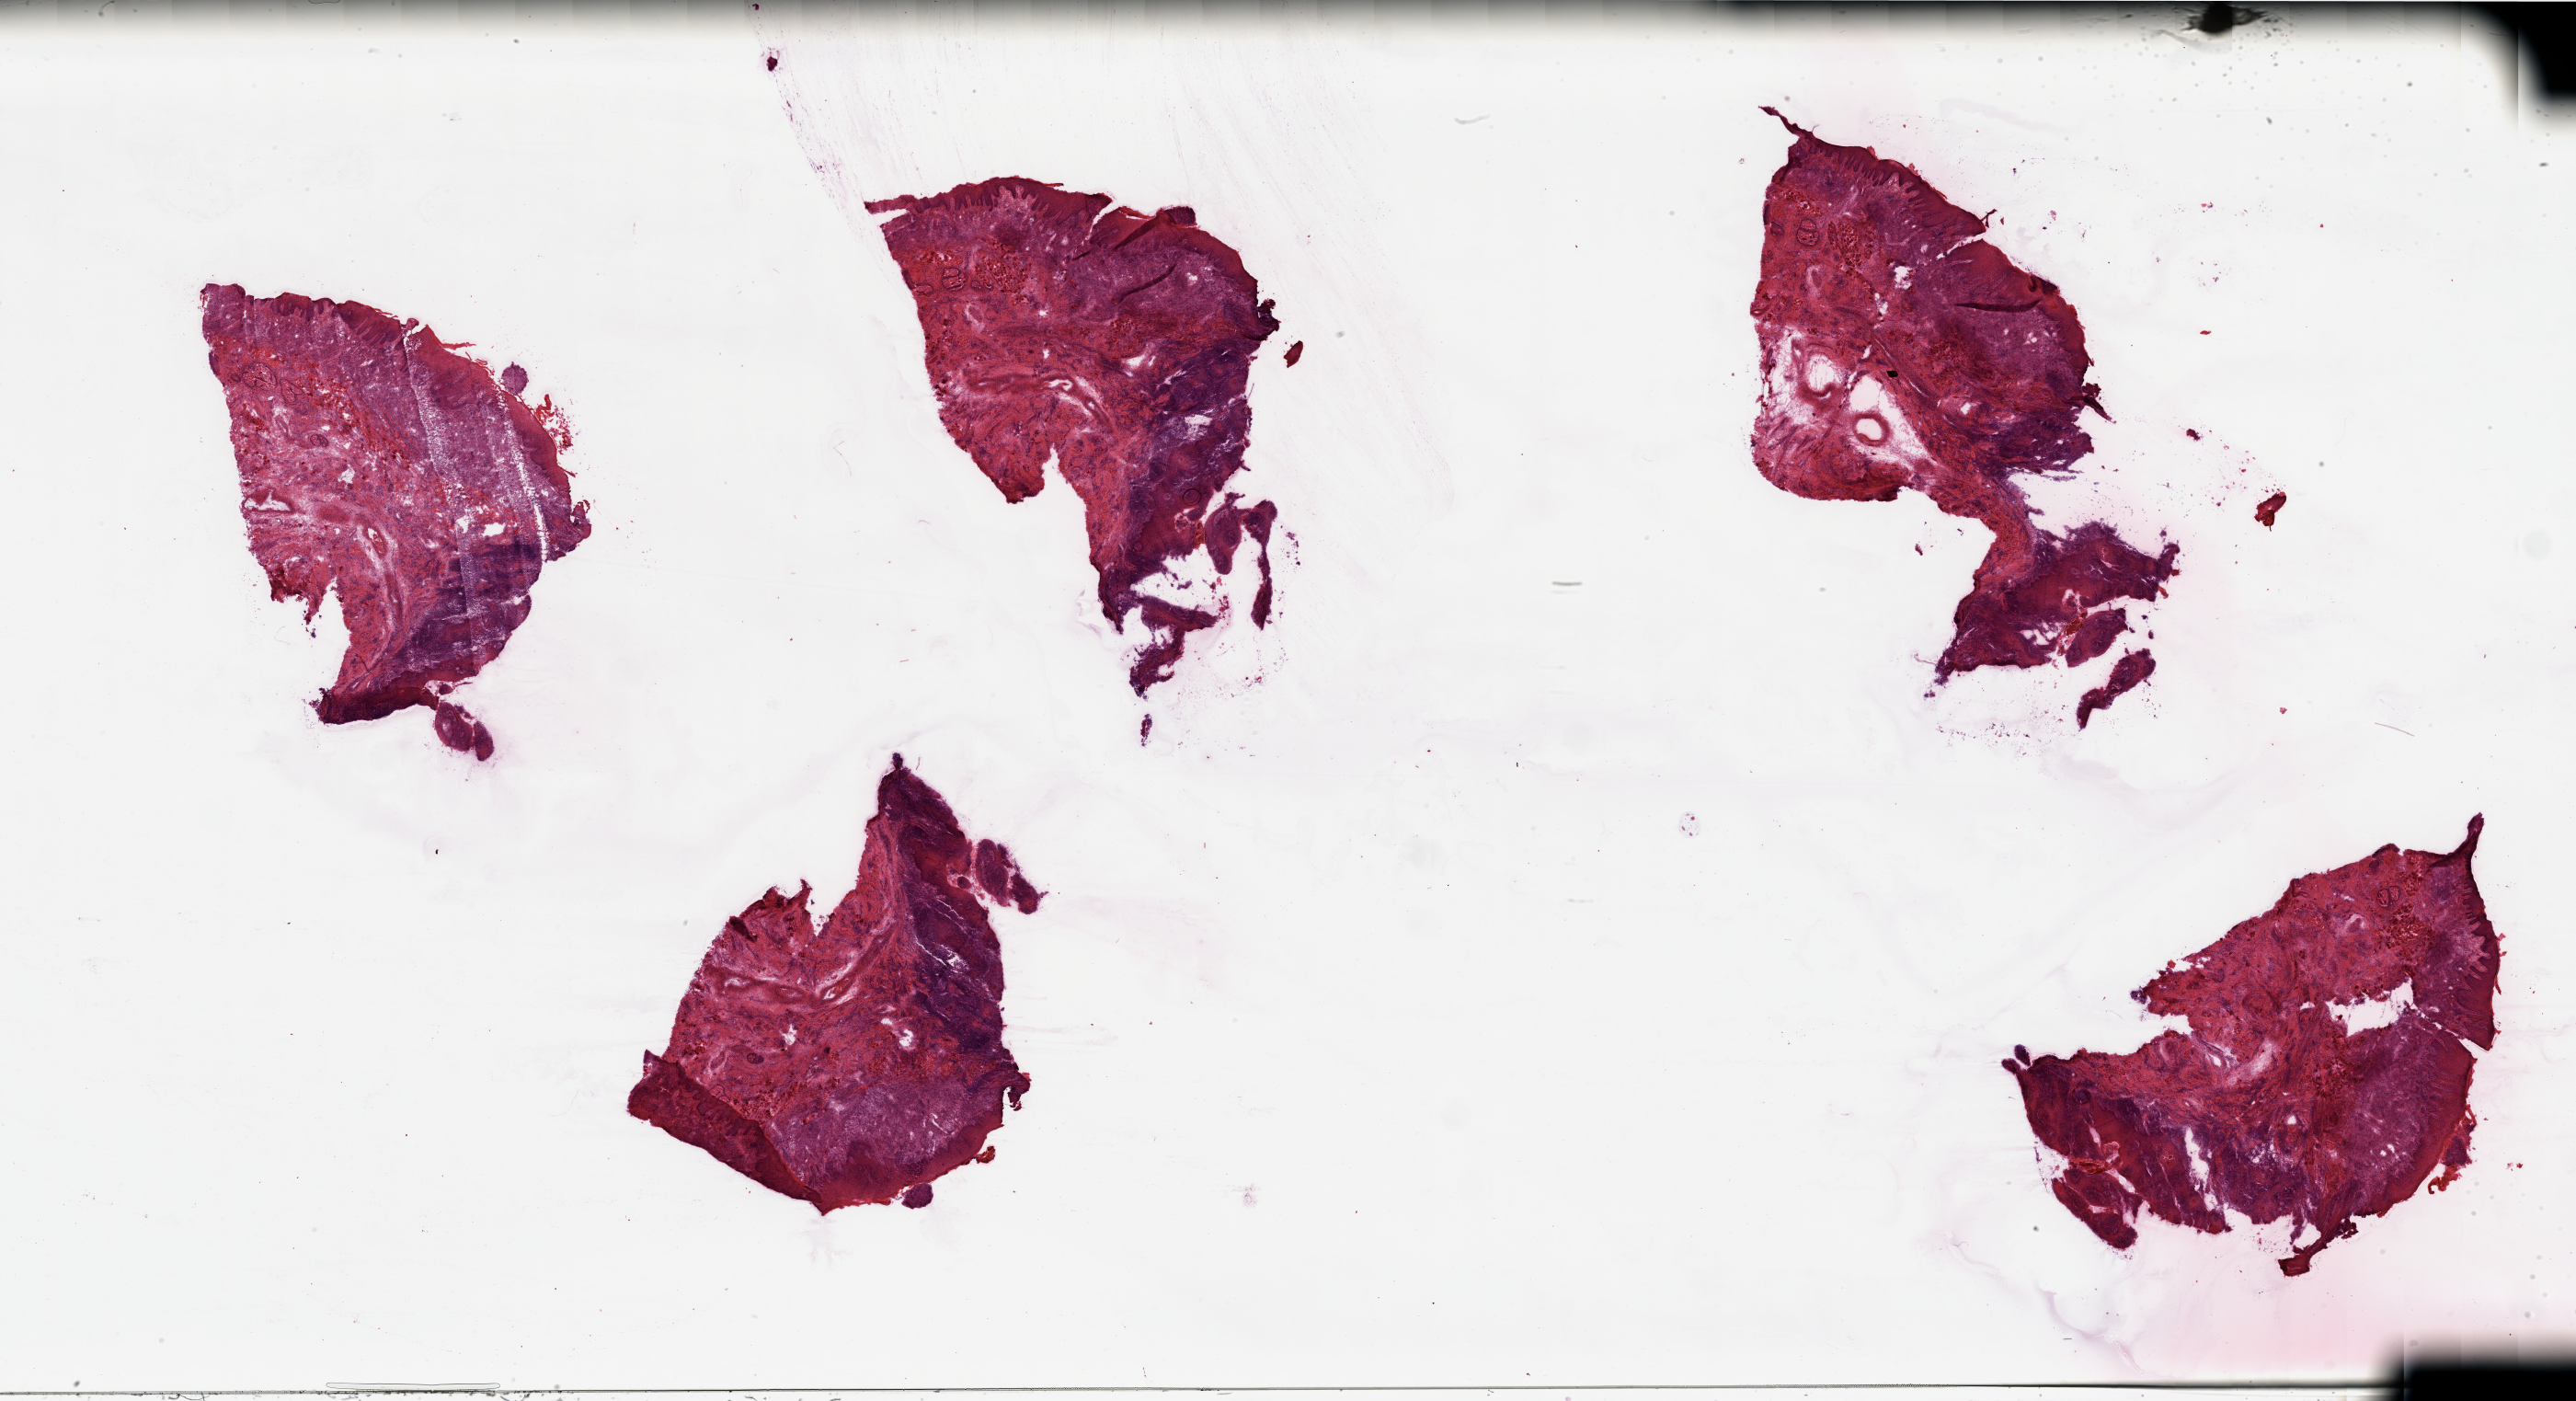
Whole-slide histology image, H&E, shown as a low-resolution overview of the whole scanned area (about 44.3 x 24.1 mm, slide scanned at 20x). Head and neck, tissue type not recorded. Male, 54 y/o.
• patient diagnosis: Squamous cell carcinoma, NOS (lip, NOS)